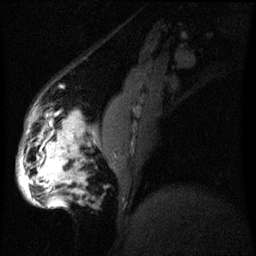
Breast MRI (dynamic contrast-enhanced), one sagittal slice; position 18 of 60 along the scan axis; dynamic contrast-enhanced series, image 2 of 3 at this slice position (ordered by acquisition); 1.5 T; TE 4.2 ms, TR 8 ms; 2.2 mm slice thickness; 256 × 256 image matrix, field of view 200 × 200 mm. Female patient, age 50 years.
Outlined on this slice (semi-automatically segmented with operator editing):
- analysis volume of interest (the breast-tissue region the enhancement analysis was run in; not a lesion): box from (x=19, y=112) to (x=89, y=209) px
- tumour enhancement mask (voxels above the 70 % enhancement threshold inside the analysis volume of interest): (x=20, y=118)–(x=74, y=207)